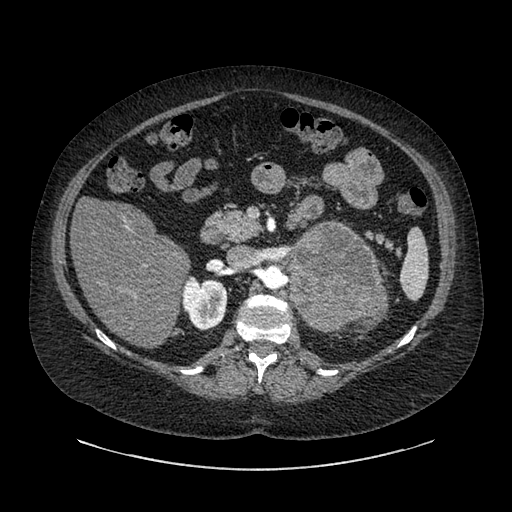
Contrast-enhanced abdominal CT, one axial slice. Slice 542 of 769 in the series (ordered by position). Reconstruction kernel SOFT. Intravenous contrast given. Soft-tissue window (W 400 / L 40 HU). 512 × 512 image matrix, field of view 460 × 460 mm. Female patient, age 61 years. Case-level facts recorded for this patient, not image findings: diagnosis: adrenocortical carcinoma; tumour side: left adrenal; tumour size at pathology: 13 cm; Ki-67 index: 79 %; stage (as recorded): 2.
Outlined on this slice (semi-automatic segmentation, software-assisted and operator-edited):
- mass: bounding box (x1, y1, x2, y2) in pixels: (290, 226, 379, 330)